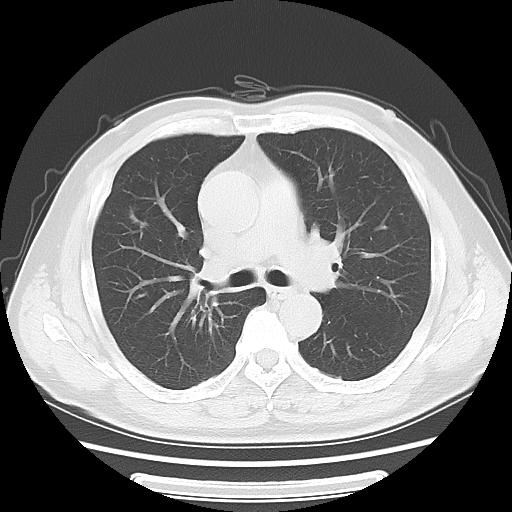
Chest CT, one axial slice. Slice 37 of 63 in the series (ordered by position). Lung window (W 1500 / L -600 HU). 5 mm slice thickness. 512 × 512 image matrix, field of view 360 × 360 mm. Patient: male, 63 years. From the clinical record (not read from this slice): clinical TNM (as recorded): T1c N0 M0.
Annotated regions visible in this slice (bounding box drawn by a radiologist):
- lung tumour (recorded histology: adenocarcinoma): box from (x=119, y=203) to (x=157, y=243) px